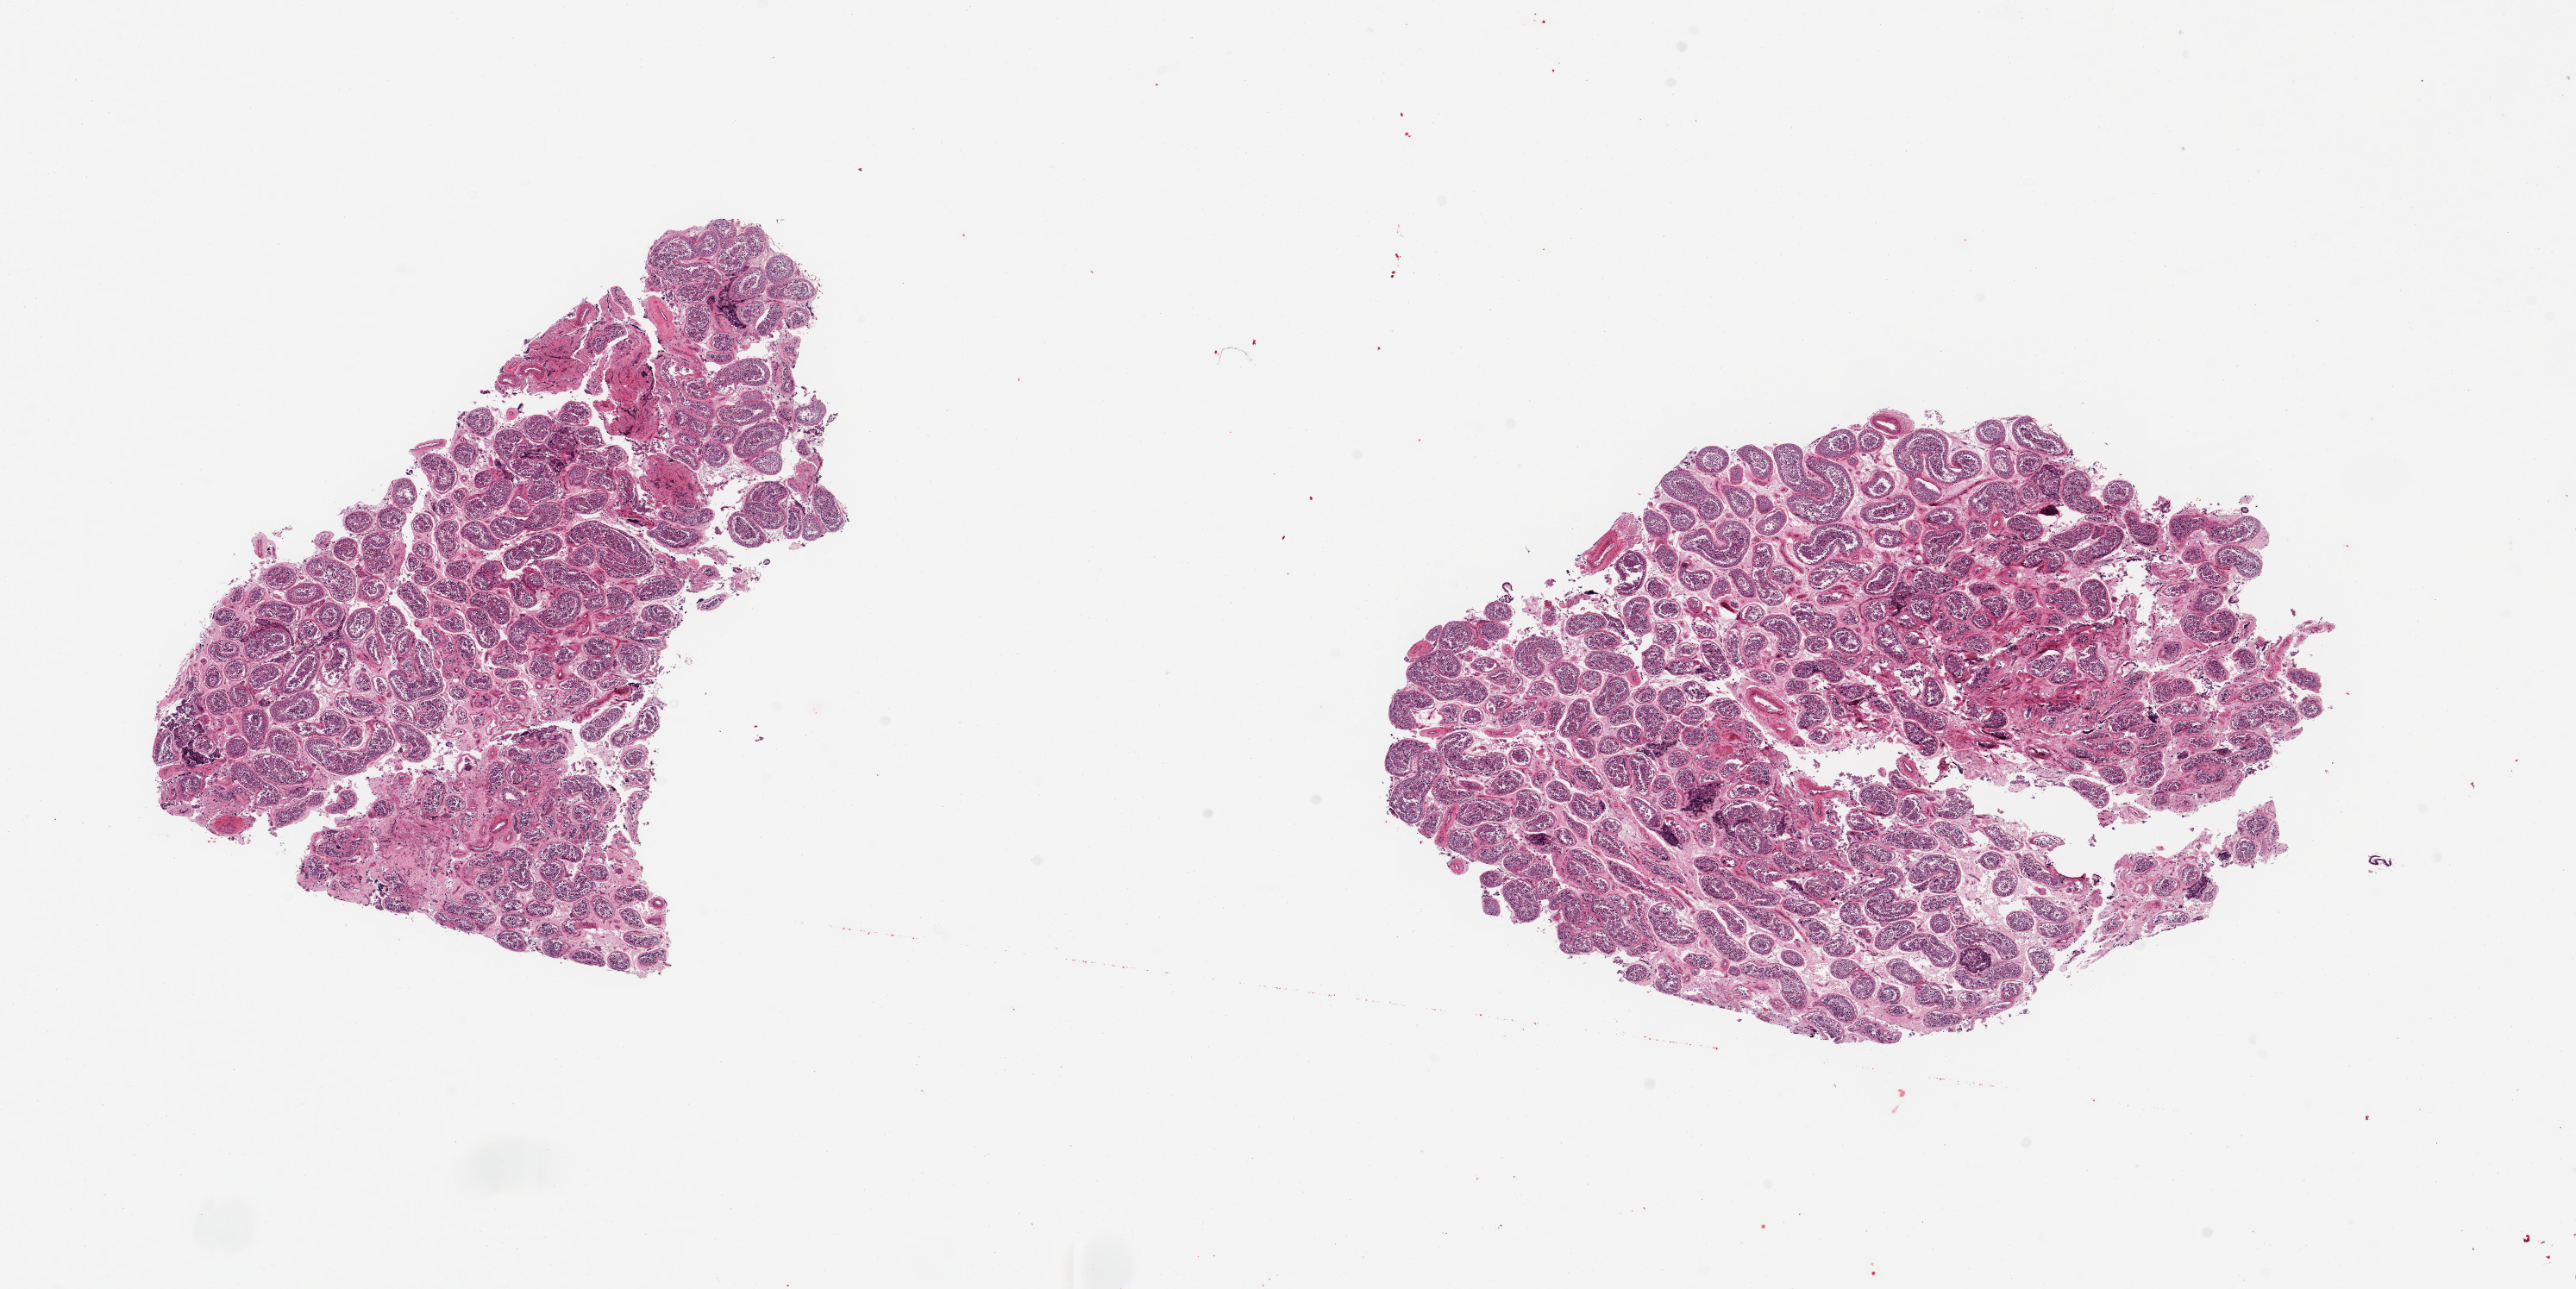
Hematoxylin and eosin (H&E) whole-slide image — whole scanned area (about 23.6 x 11.8 mm) shown as a low-resolution overview, PAXgene-fixed paraffin-embedded (PFPE) section, section of testis (target tissue), tissue donor sample.
Pathologist's review note for this sample: 2 pieces, no abnormalities.